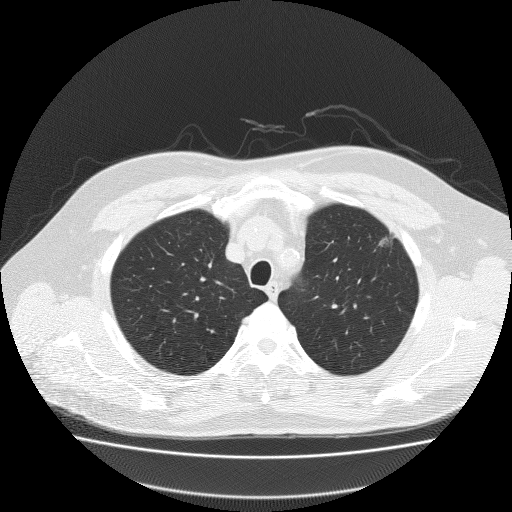
Low-dose screening chest CT, one axial slice; position 163 of 204 along the scan axis; lung window (W 1500 / L -600 HU); 512 × 512 image matrix, field of view 410 × 410 mm.
Annotated regions visible in this slice (expert manual segmentation):
- lesion 1 (tumor, upper lobe of left lung): box from (x=378, y=236) to (x=391, y=248) px